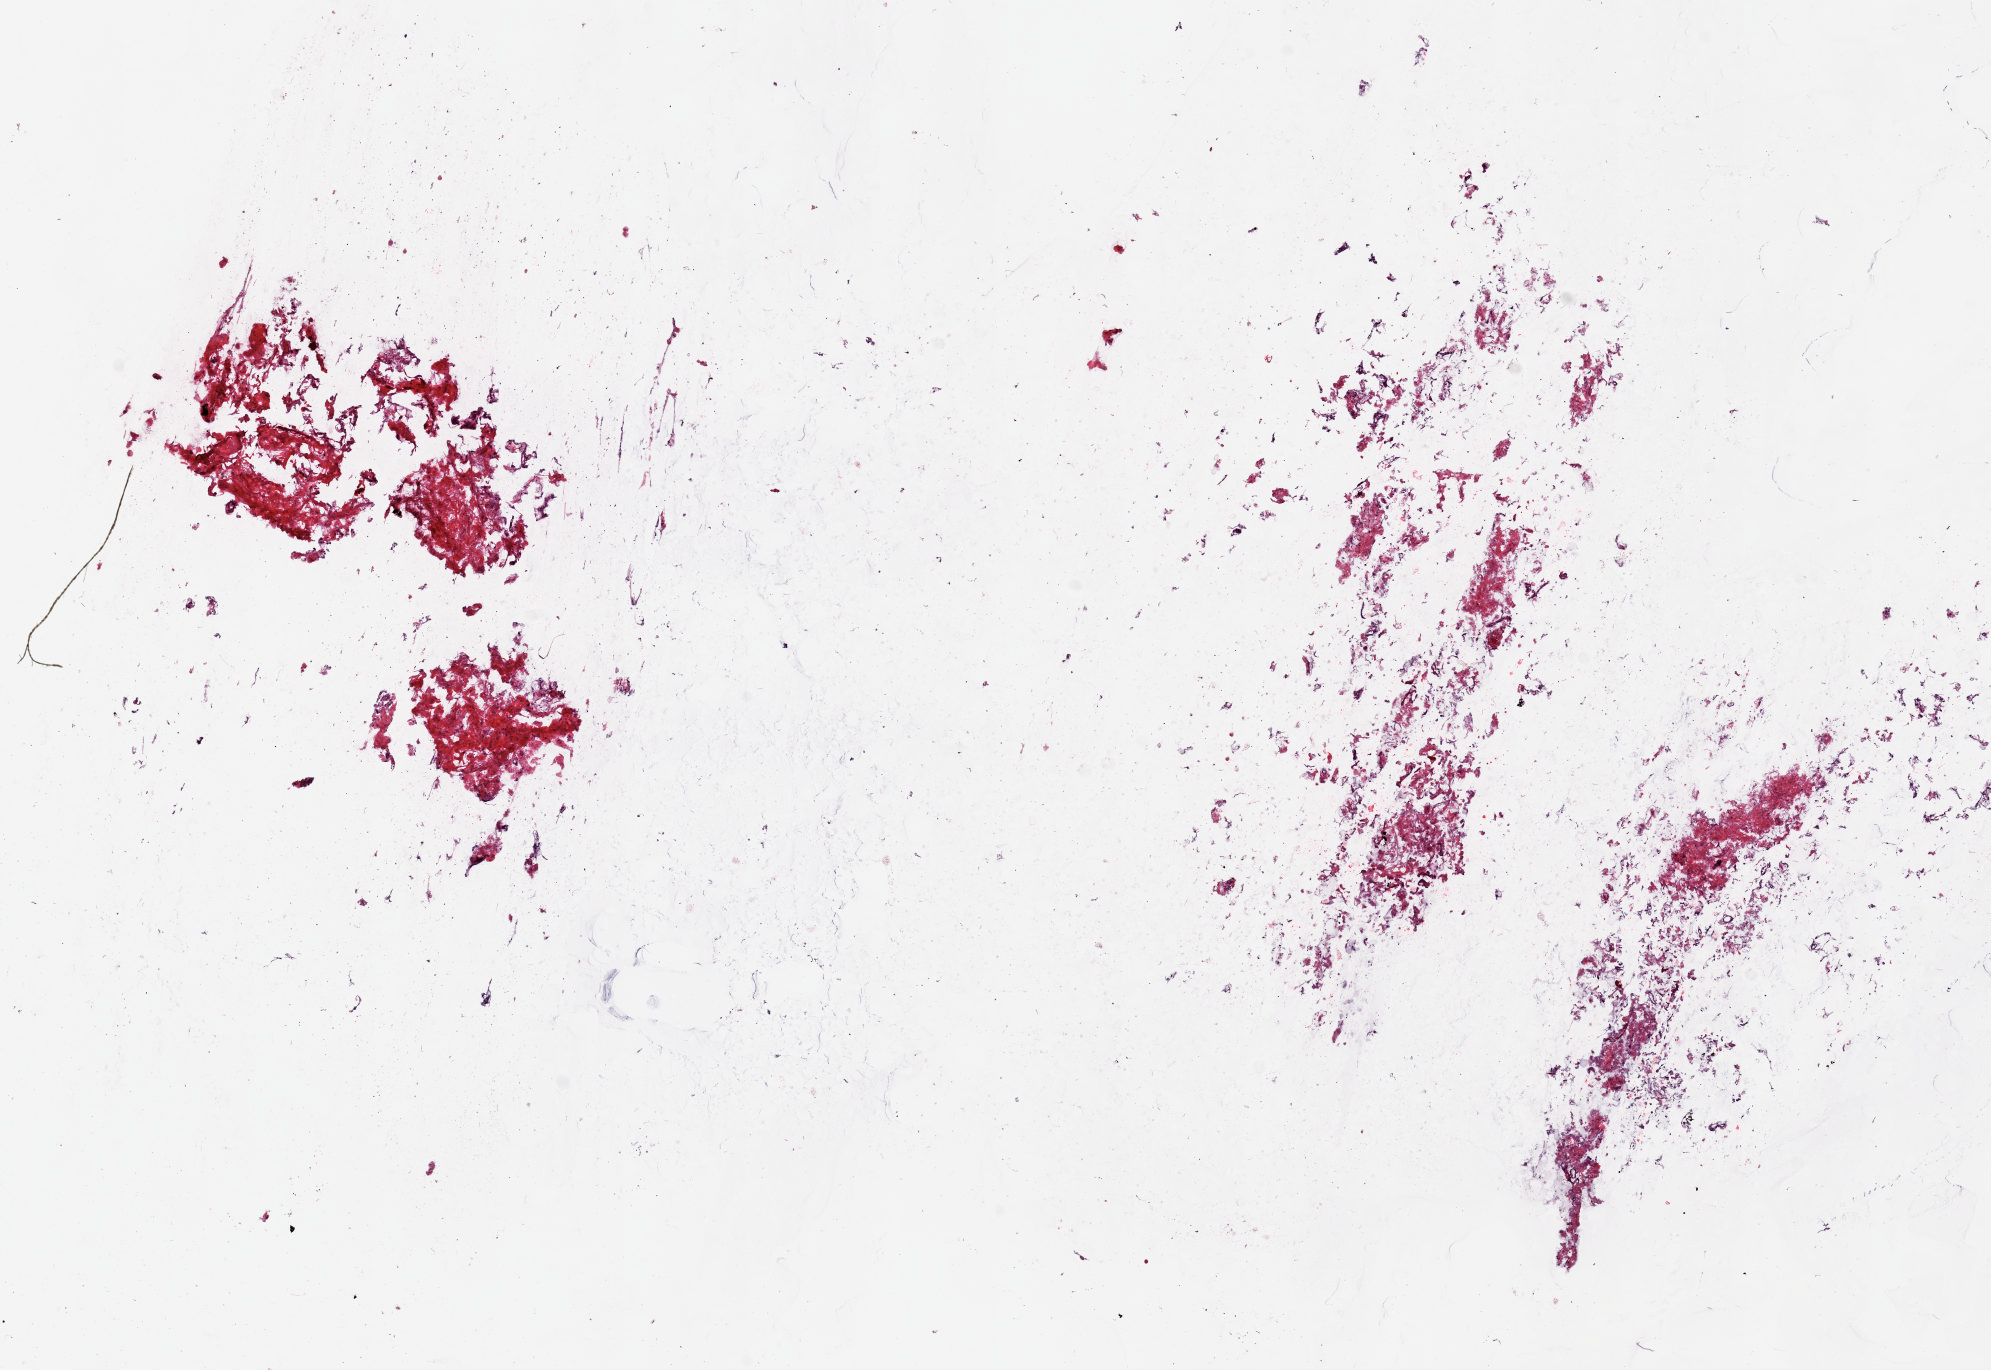
H&E-stained whole-slide image — shown as a low-resolution overview of the whole scanned area (about 15.7 x 10.8 mm). Frozen section from the top of the tissue portion. Breast, solid tissue normal (non-tumour tissue) sample. Female, age 62 years at initial diagnosis. Slide review estimates, as recorded: tumour cells 0%, tumour nuclei 0%, normal cells 0%, stromal cells 100%, necrosis 0%. Inflammatory infiltration, as recorded: lymphocyte infiltration 0%, monocyte infiltration 0%, neutrophil infiltration 0%.
This section: solid tissue normal sample (biorepository sample class). Patient diagnosis: Lobular carcinoma, NOS.